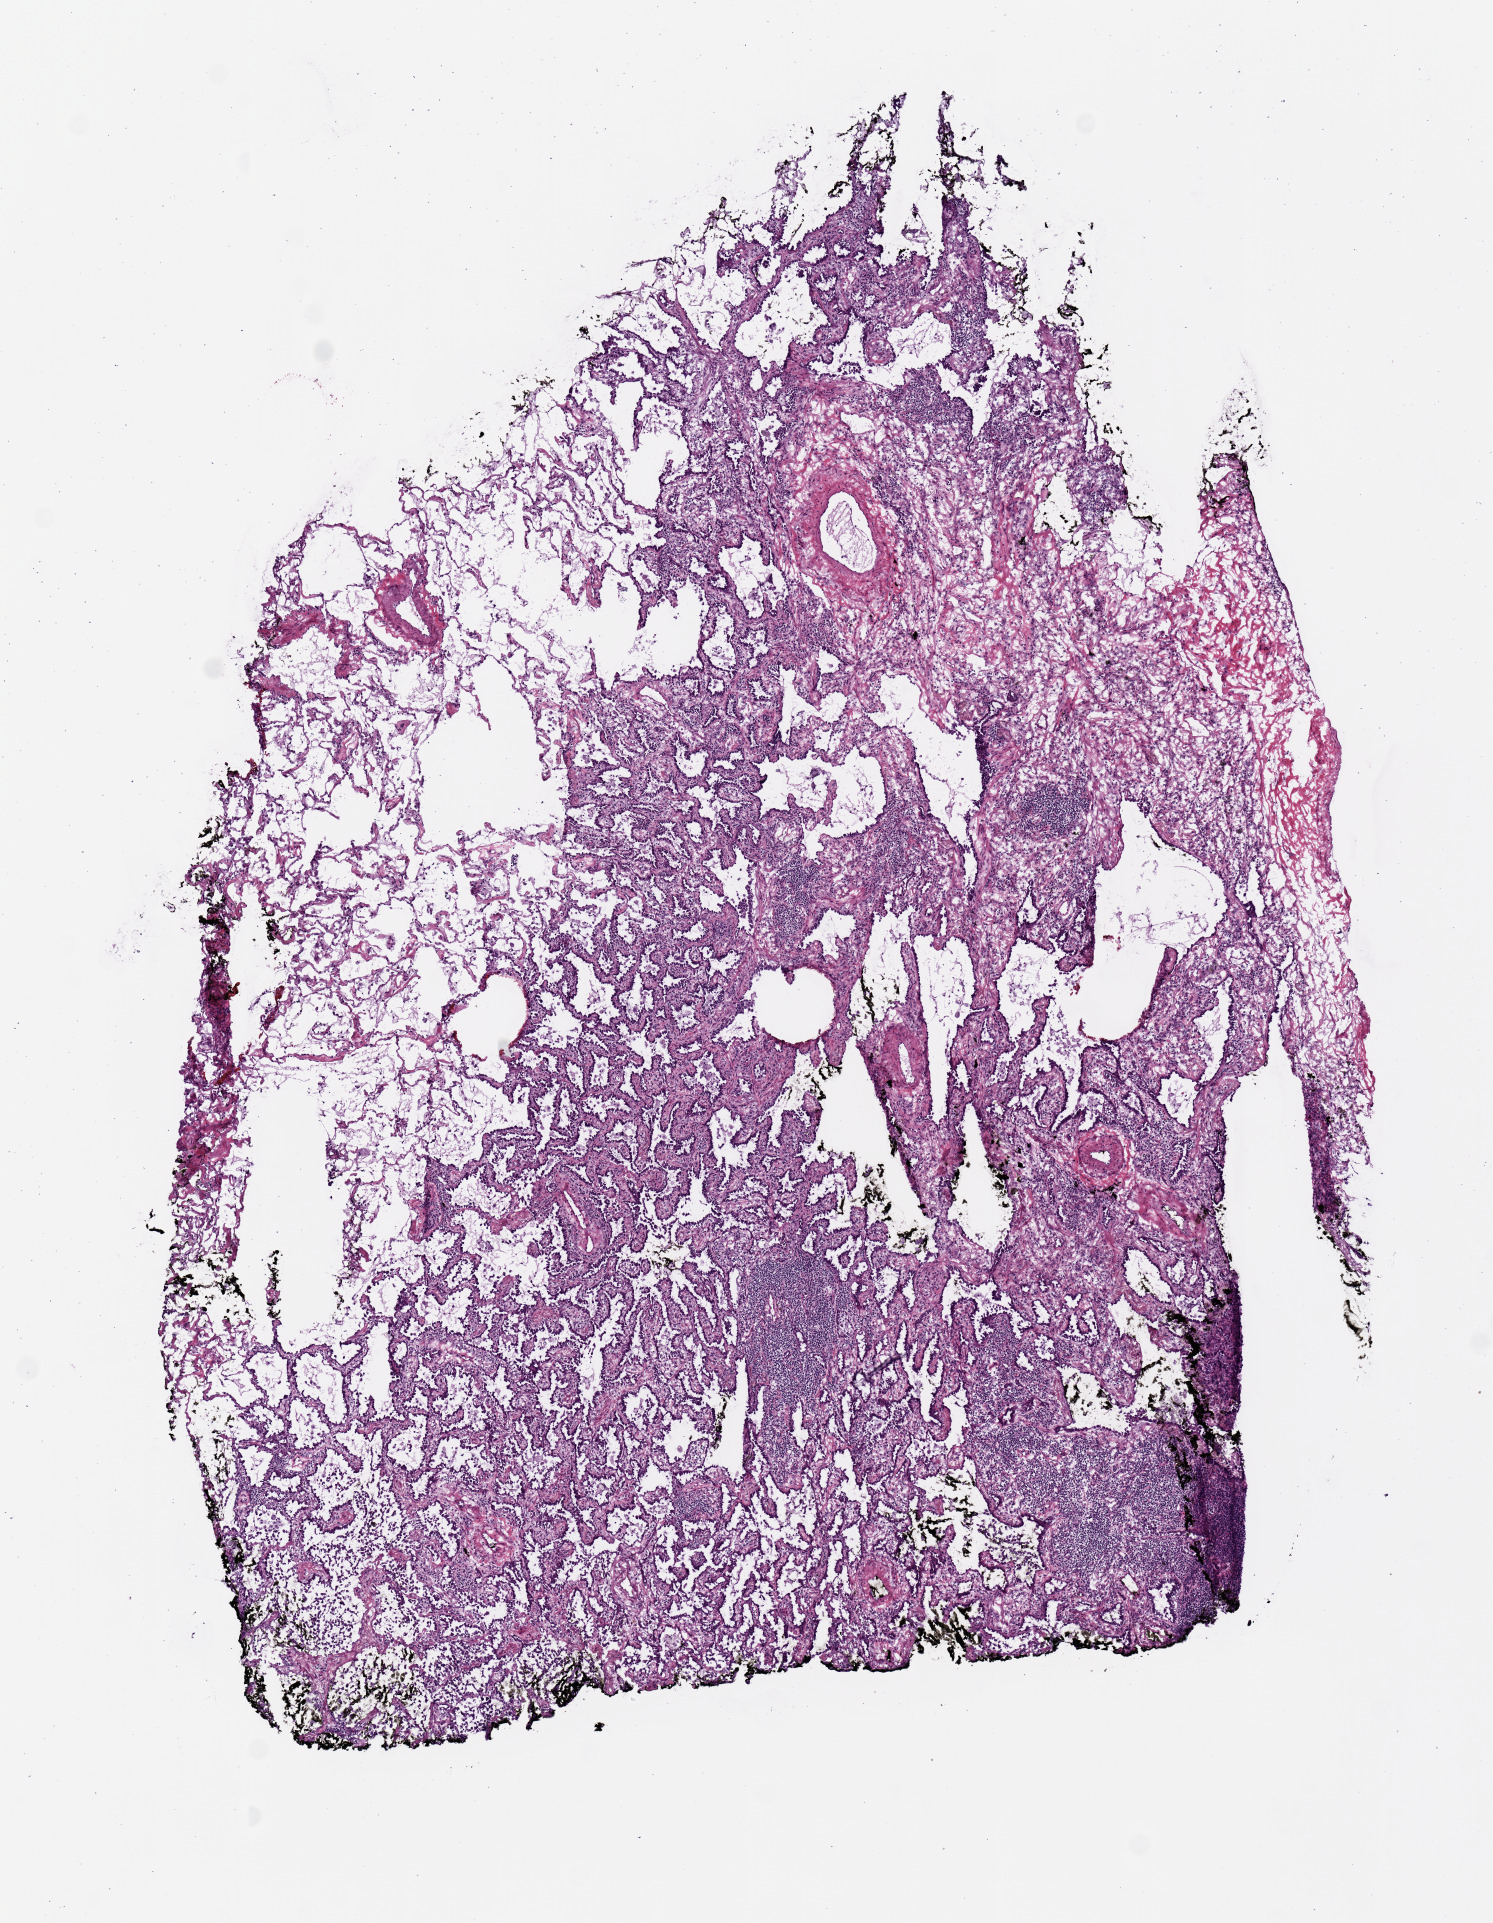
Digitized Hematoxylin and eosin (H&E) stained tissue section (whole slide) — a low-resolution overview of the entire scanned area, about 5.9 x 7.6 mm, frozen section from the top of the tissue portion, lung, primary tumour sample. Female patient; age at initial diagnosis 60 years. Slide review estimates, as recorded: tumour cells 83%, tumour nuclei 65%, normal cells 2%, stromal cells 15%, necrosis 0%.
Laterality: right. AJCC pathologic stage: IA. Histologic diagnosis: Adenocarcinoma, NOS (upper lobe, lung).